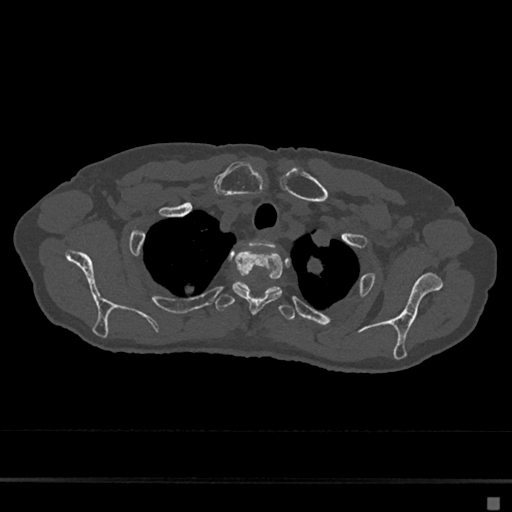
CT including the spine, one axial slice; slice 566 of 797 in the series (ordered by position); reconstruction kernel Br40s/3; 120 kVp; bone window (W 1800 / L 400 HU); 512 × 512 image matrix, field of view 360 × 360 mm. Female patient, age 68 years. Case-level facts recorded for this patient, not image findings: primary cancer: renal.
Outlined on this slice (semi-automatic segmentation, software-assisted and operator-edited):
- T1 vertebra: box from (x=251, y=239) to (x=276, y=248) px
- T2 vertebra: (x=232, y=250)–(x=283, y=314)
- T3 vertebra: (x=215, y=281)–(x=296, y=321)